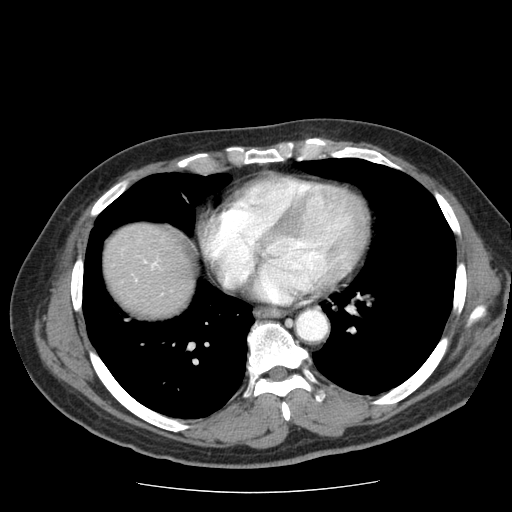
Contrast-enhanced abdominal CT (liver protocol), one axial slice. Position 73 of 85 along the scan axis. Reconstruction kernel STANDARD. 120 kVp. Soft-tissue window (W 400 / L 40 HU). 2.5 mm slice thickness. 512 × 512 image matrix, field of view 360 × 360 mm. From the clinical record (not read from this slice): diagnosis: hepatocellular carcinoma (patient treated with transarterial chemoembolisation; whether this scan precedes or follows treatment is not stated here); TNM stage (as recorded): Stage-IIIA; Child-Pugh class: A.
Outlined on this slice (semi-automatic segmentation, software-assisted and operator-edited):
- liver parenchyma outside the tumour (the mass and vessels are separate outlines, so this box may not span the whole liver): bounding box [x1, y1, x2, y2] px = [104, 222, 194, 316]
- liver vessels: [144, 261, 158, 267]